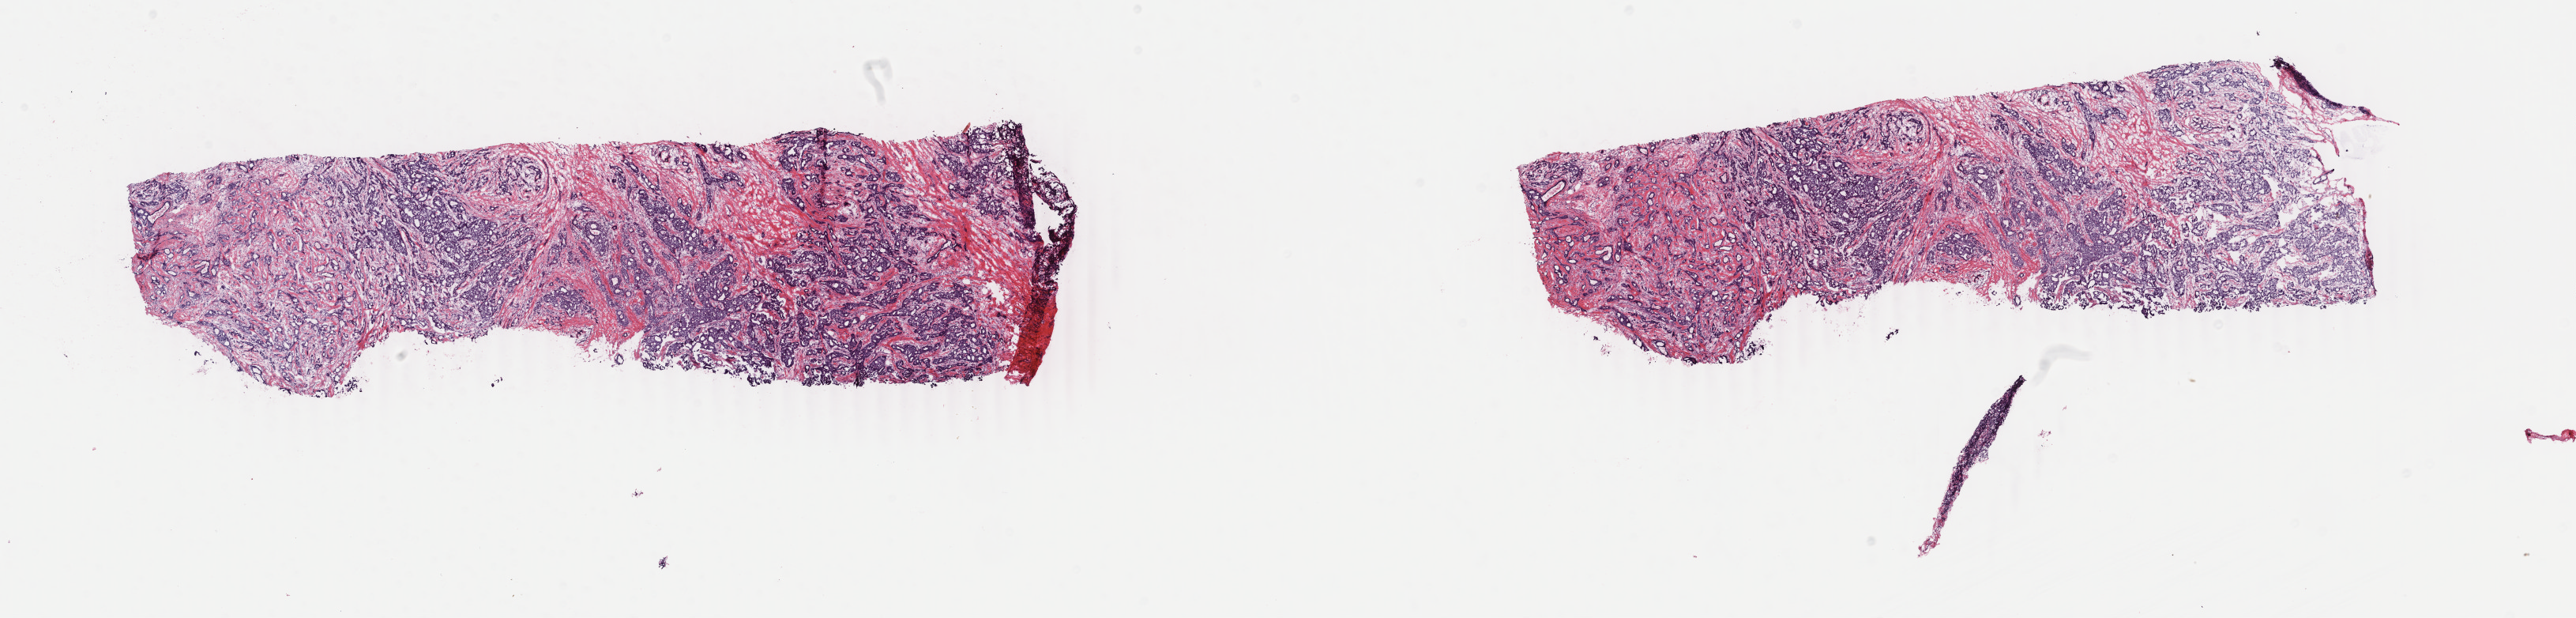
Digitized H&E-stained tissue section (whole slide) — a low-resolution overview of the entire scanned area, about 25.9 x 6.2 mm (acquisition: 40x scan). Frozen section. Primary tumour sample from the breast. Patient: female, age at initial diagnosis 39 years. Slide review estimates, as recorded: tumour cells 75%, tumour nuclei 75%, normal cells 0%, stromal cells 25%, necrosis 0%. Infiltration values recorded for this section: lymphocyte infiltration 30%, monocyte infiltration 10%, neutrophil infiltration 30%.
* AJCC pathologic stage: IIA
* laterality: left
* diagnosis: Infiltrating duct carcinoma, NOS